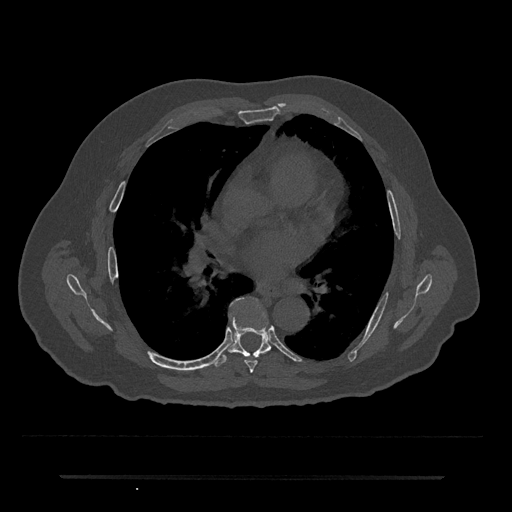
CT including the spine, one axial slice; slice 409 of 797 in the series (ordered by position); 120 kVp; bone window (W 1800 / L 400 HU); 512 × 512 image matrix. Male patient, age 69 years. From the clinical record (not read from this slice): primary cancer: prostate.
Annotated regions visible in this slice (semi-automatically segmented with operator editing):
- T6 vertebra: bounding box <245,360,257,373> (left, top, right, bottom; pixels)
- T7 vertebra: <214,304,272,367>